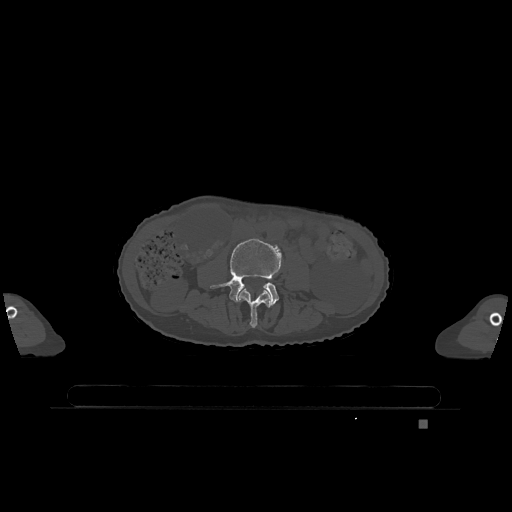
CT including the spine, one axial slice; slice 322 of 1317 in the series (ordered by position); bone window (W 1800 / L 400 HU); 0.5 mm slice thickness; 512 × 512 image matrix, field of view 500 × 500 mm. Female patient, age 74 years. Case-level facts recorded for this patient, not image findings: primary cancer: lung; vertebrae with lytic lesions (as recorded): T1, T4, T5, T6, L4, L5.
Structures marked on this image (semi-automatic segmentation, software-assisted and operator-edited):
- L3 vertebra: bounding box <238,289,271,328> (left, top, right, bottom; pixels)
- L4 vertebra: <210,238,282,306>